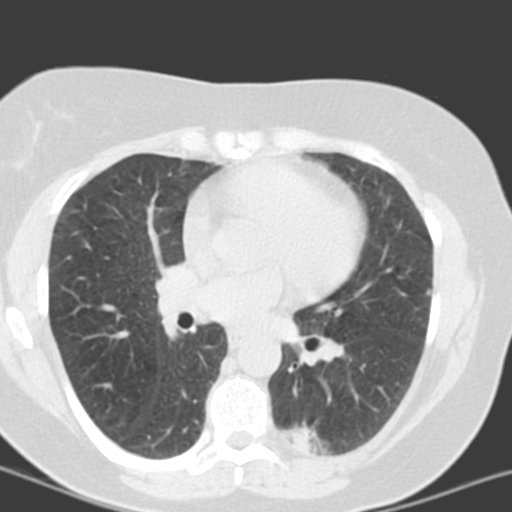
Low-dose screening chest CT, one axial slice. Slice 83 of 150 in the series (ordered by position). 120 kVp. Lung window (W 1500 / L -600 HU). 3.2 mm slice thickness. 512 × 512 image matrix, field of view 290 × 290 mm.
Outlined on this slice (expert manual segmentation):
- lesion 2 (tumor, lower lobe of left lung): bounding box [x1, y1, x2, y2] px = [293, 428, 316, 449]